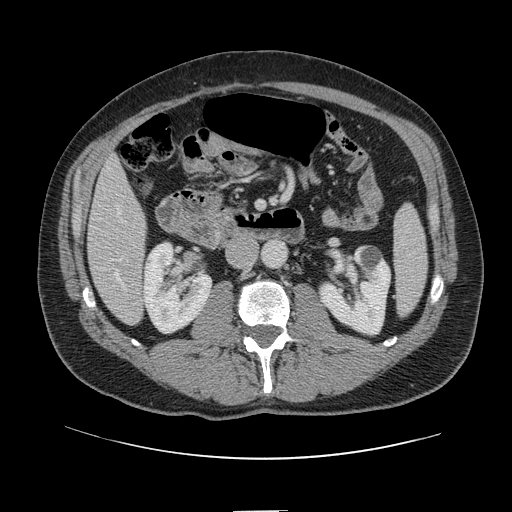
Contrast-enhanced abdominal CT, one axial slice; position 34 of 161 along the scan axis; 120 kVp; intravenous contrast given; soft-tissue window (W 400 / L 40 HU); 2.5 mm slice thickness; 512 × 512 image matrix. Male patient, age 66 years. From the clinical record (not read from this slice): diagnosis: colorectal cancer liver metastases, imaged before liver resection; multiple liver metastases: no; largest metastasis: 3.5 cm.
Outlined on this slice (outlined manually by an expert reader):
- hepatic veins: bounding box (x1, y1, x2, y2) in pixels: (116, 211, 125, 287)
- liver: (88, 160, 147, 324)
- planned liver remnant (the part of the liver to remain after resection): (88, 159, 145, 264)